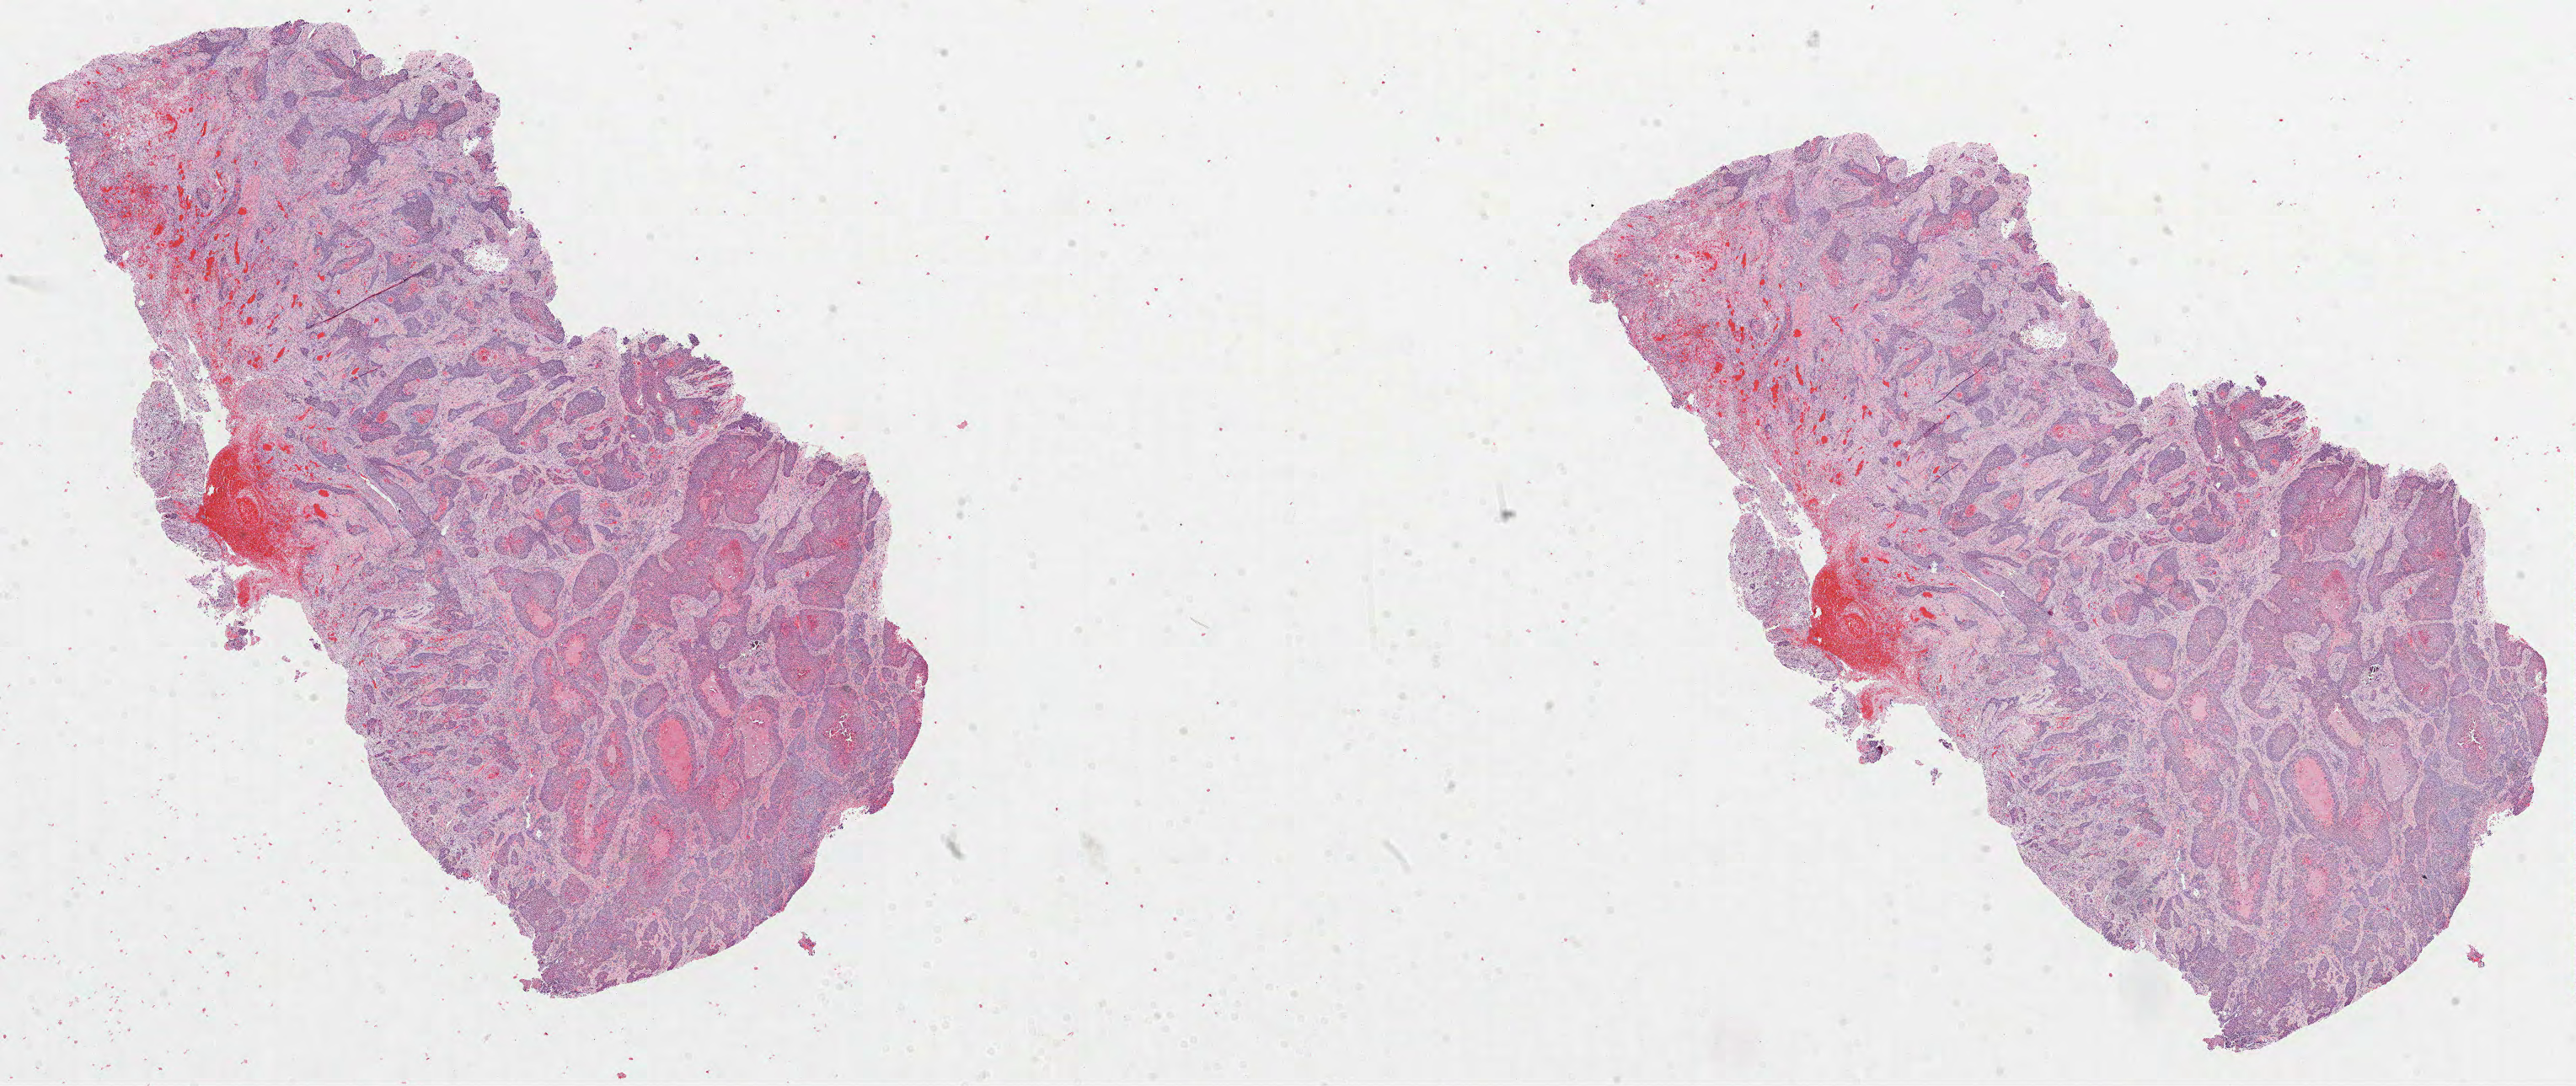
Digitized Hematoxylin and eosin (H&E) stained tissue section (whole slide) — low-resolution overview of the scanned area, about 24.7 x 10.4 mm (from a 40x scan). FFPE section. Primary tumour sample from the head and neck. Male patient; age at initial diagnosis 64 years. Histologic grade: G2 (moderately differentiated).
- AJCC pathologic stage: IVA (7th edition)
- pathologic diagnosis: Squamous cell carcinoma, NOS (larynx, NOS)